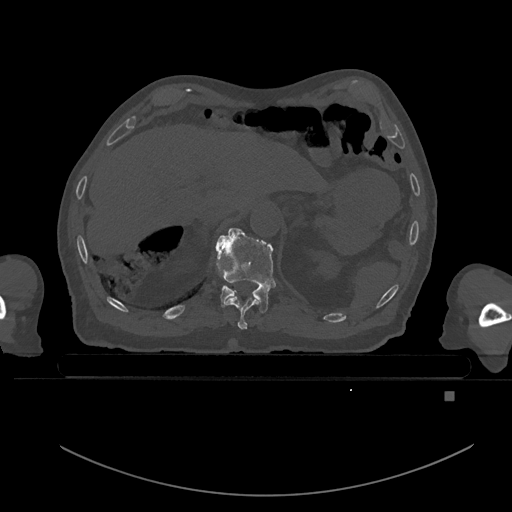
CT including the spine, one axial slice; position 53 of 969 along the scan axis; bone window (W 1800 / L 400 HU); 512 × 512 image matrix, field of view 456 × 456 mm. Male patient, age 82 years. Case-level facts recorded for this patient, not image findings: primary cancer: prostate; vertebrae with lytic lesions (as recorded): T11, T9, T8, T2.
Outlined on this slice (semi-automatically segmented with operator editing):
- T10 vertebra: bounding box (x1, y1, x2, y2) in pixels: (225, 296, 259, 330)
- T11 vertebra: (216, 227, 275, 313)